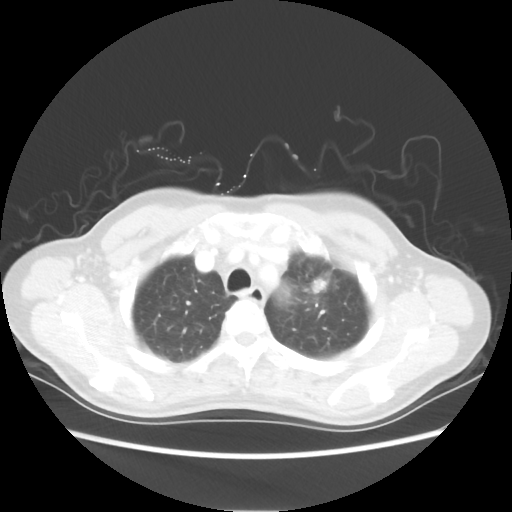
Chest CT, one axial slice; position 44 of 54 along the scan axis; lung window (W 1500 / L -600 HU); 5 mm slice thickness; 512 × 512 image matrix. Female patient, age 53 years. From the clinical record (not read from this slice): clinical TNM (as recorded): T1c N0 M0.
Annotated regions visible in this slice (rectangle marked by the reading radiologist):
- lung tumour (recorded histology: adenocarcinoma): box from (x=303, y=267) to (x=330, y=303) px
- lung tumour (recorded histology: adenocarcinoma): (x=311, y=271)–(x=332, y=297)